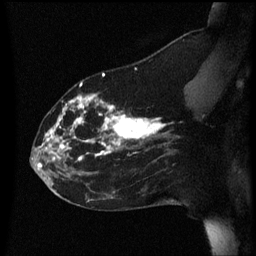
Breast MRI (dynamic contrast-enhanced), one sagittal slice; position 21 of 60 along the scan axis; dynamic contrast-enhanced series, image 2 of 3 at this slice position (ordered by acquisition); 1.5 T; TE 4.2 ms, TR 8.4 ms; 256 × 256 image matrix. Patient: female, 35 years. From the clinical record (not read from this slice): setting: breast cancer imaged before/during neoadjuvant chemotherapy; receptor status: HER2-positive.
Structures marked on this image (semi-automatically segmented with operator editing):
- analysis volume of interest (the breast-tissue region the enhancement analysis was run in; not a lesion): box from (x=31, y=72) to (x=178, y=173) px
- tumour enhancement mask (voxels above the 70 % enhancement threshold inside the analysis volume of interest): (x=39, y=74)–(x=172, y=167)